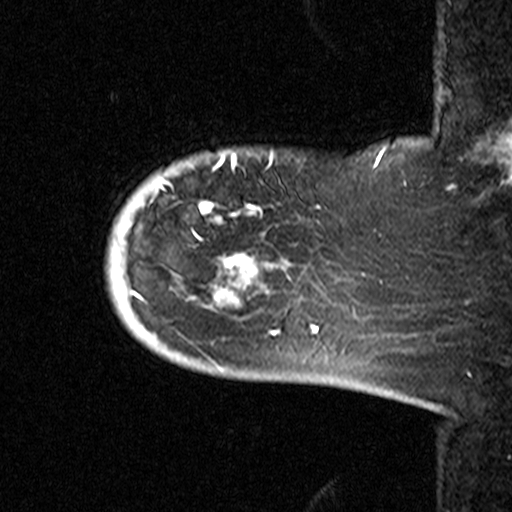
Breast MRI (dynamic contrast-enhanced), one sagittal slice. Slice 6 of 44 in the series (ordered by position). Dynamic contrast-enhanced study with each time point stored as its own series, time point 2 of 3 at this slice position (early post-contrast, ordered by acquisition time). 1.5 T. TE 4.5 ms, TR 11 ms. 512 × 512 image matrix. Patient: female, 53 years. From the clinical record (not read from this slice): setting: breast cancer imaged before/during neoadjuvant chemotherapy; receptor status: HR-positive, HER2-negative.
Outlined on this slice (semi-automatic segmentation, software-assisted and operator-edited):
- analysis volume of interest (the breast-tissue region the enhancement analysis was run in; not a lesion): bounding box (x1, y1, x2, y2) in pixels: (96, 154, 311, 367)
- tumour enhancement mask (voxels above the 90 % enhancement threshold inside the analysis volume of interest): (132, 154, 280, 335)